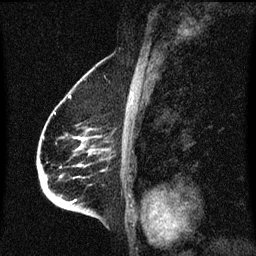
Breast MRI (dynamic contrast-enhanced), one sagittal slice; position 41 of 60 along the scan axis; dynamic contrast-enhanced series, image 2 of 3 at this slice position (ordered by acquisition); 1.5 T; TE 4.2 ms, TR 8.4 ms; 2 mm slice thickness; 256 × 256 image matrix, field of view 200 × 200 mm. Female patient, age 68 years. Case-level facts recorded for this patient, not image findings: setting: breast cancer imaged before/during neoadjuvant chemotherapy; receptor status: triple-negative.
Annotated regions visible in this slice (semi-automatic segmentation, software-assisted and operator-edited):
- analysis volume of interest (the breast-tissue region the enhancement analysis was run in; not a lesion): box from (x=39, y=96) to (x=113, y=213) px
- tumour enhancement mask (voxels above the 70 % enhancement threshold inside the analysis volume of interest): (x=68, y=138)–(x=76, y=205)